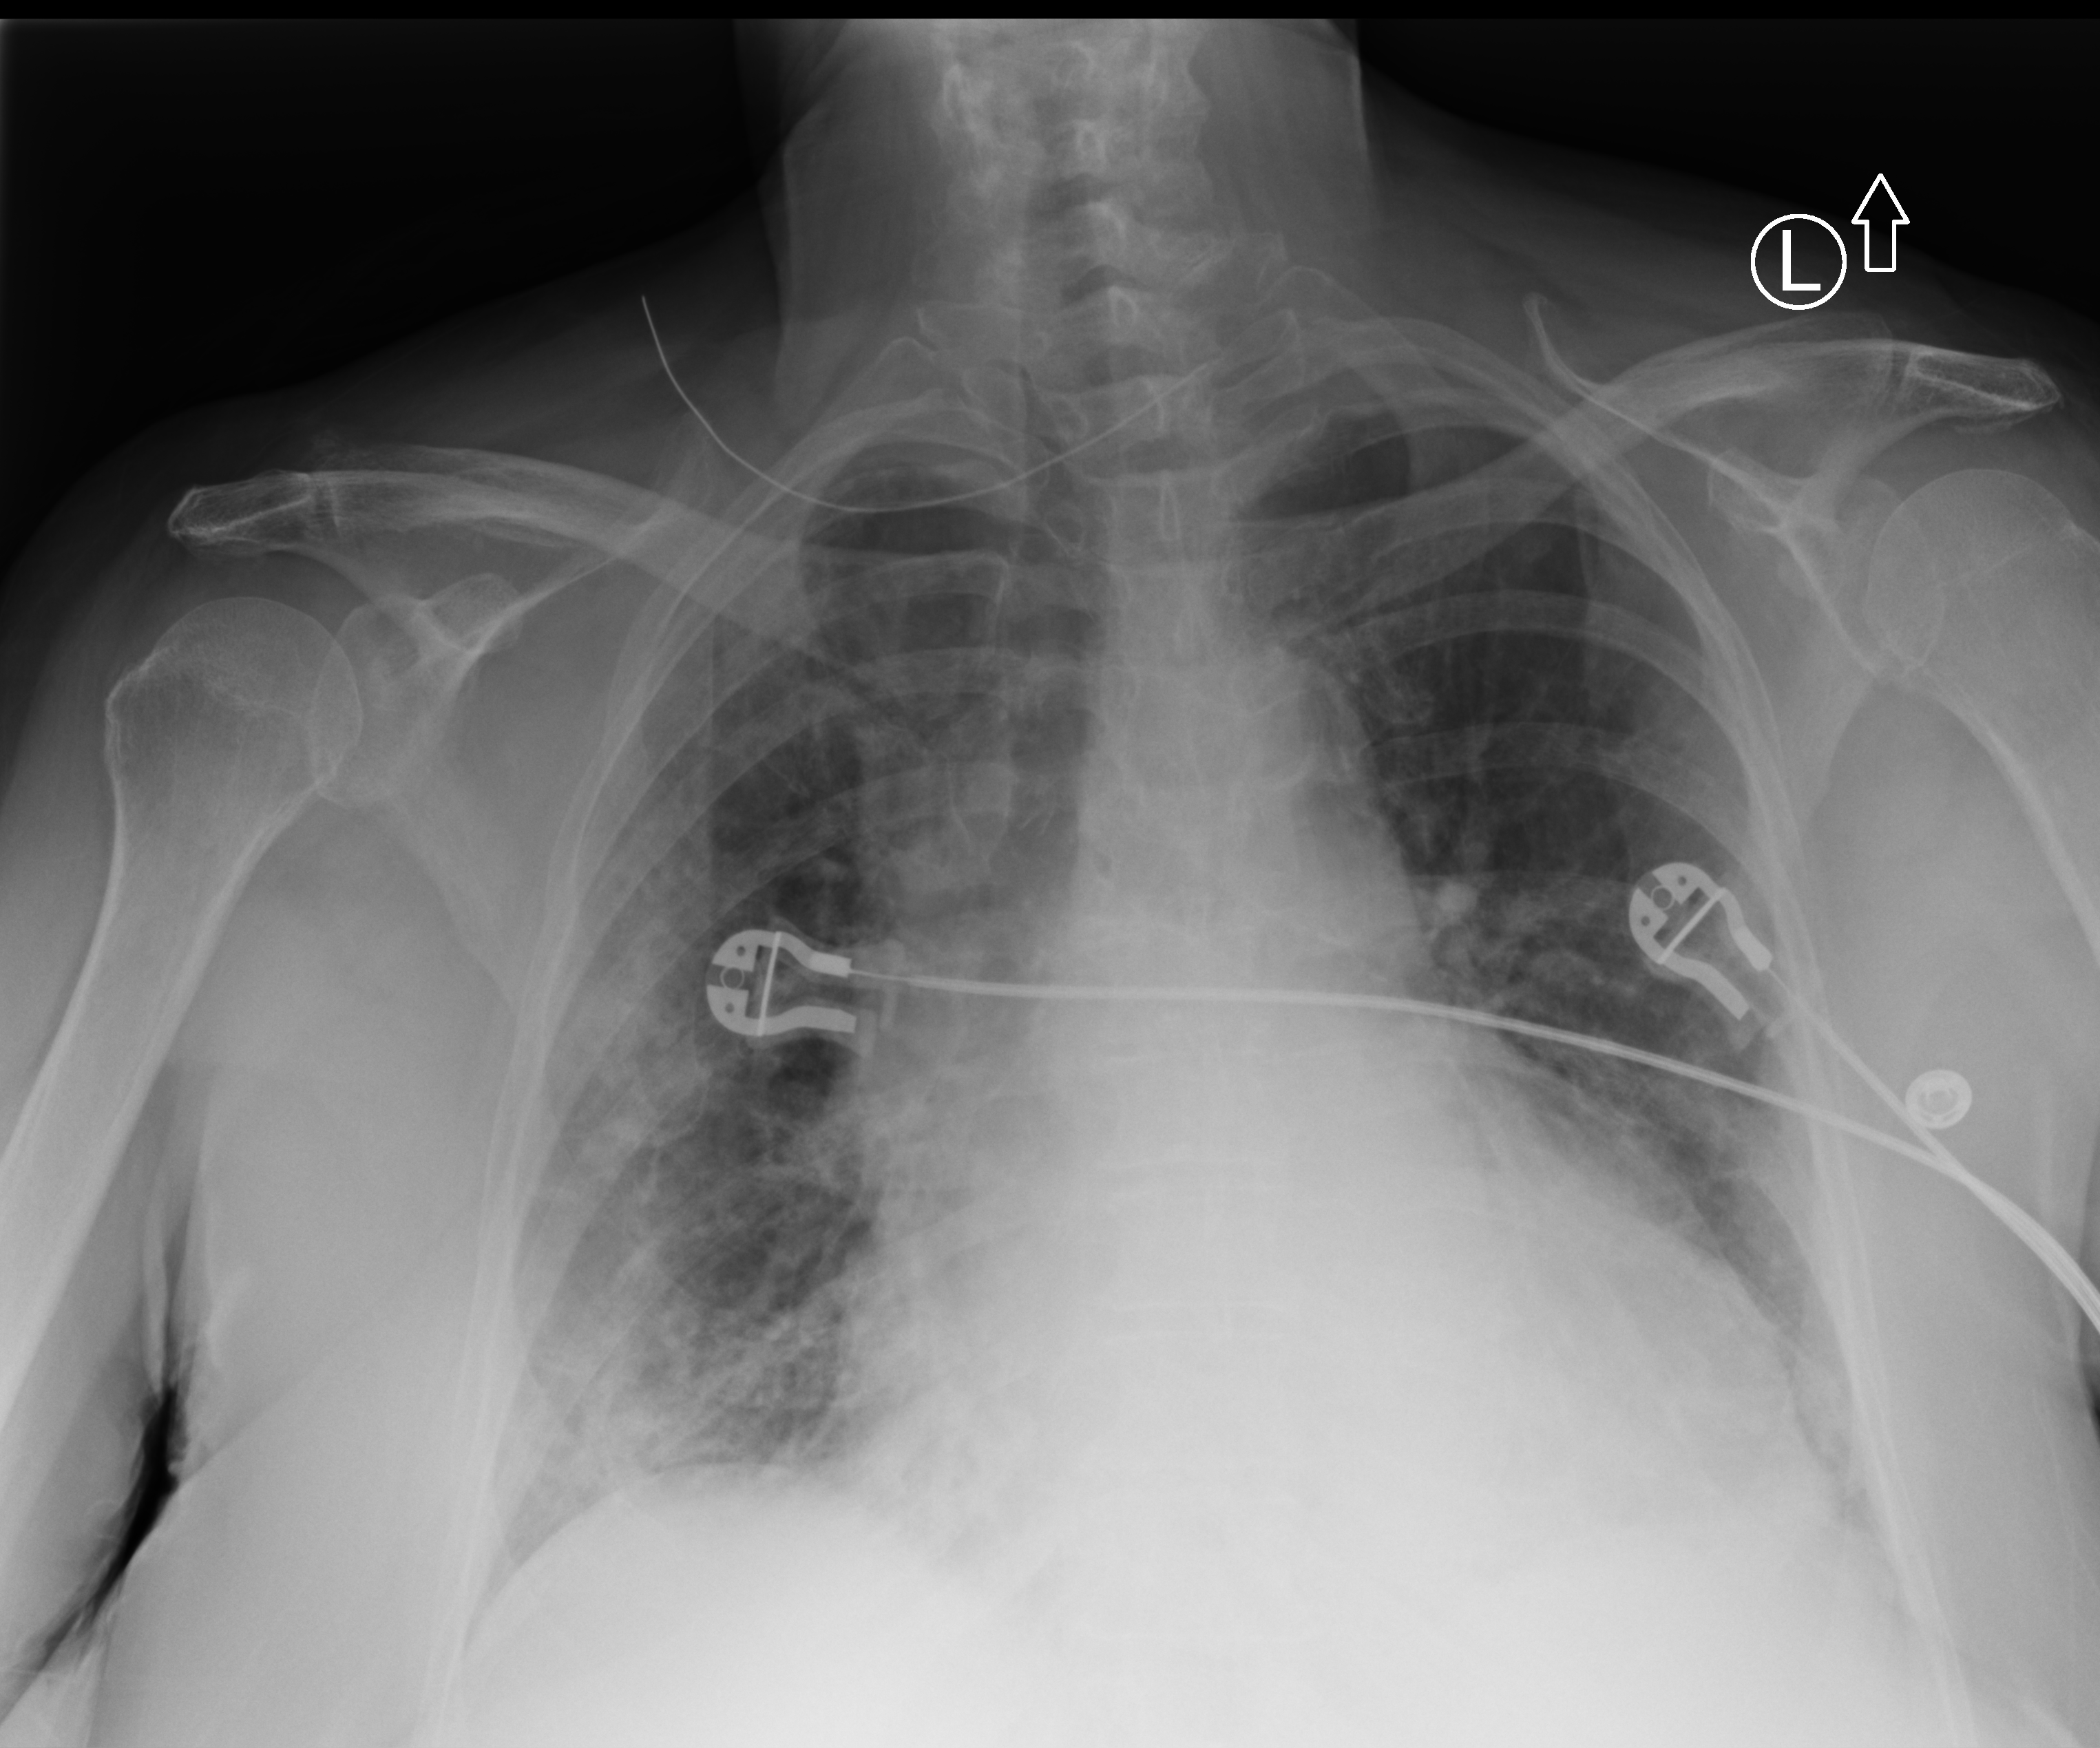
Chest X-ray (portable); anteroposterior (AP) projection. Patient hospitalised with COVID-19; female, aged 75–90 years.
From the hospital-stay record, not from the radiograph (when in the stay this image was taken is not recorded): mechanically ventilated during this hospital stay: no; admitted to intensive care during this hospital stay: no; length of hospital stay: 11 days.